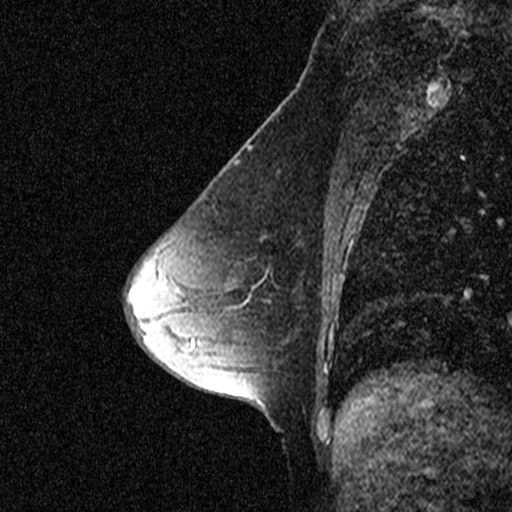
Breast MRI (dynamic contrast-enhanced), one sagittal slice; dynamic contrast-enhanced study with each time point stored as its own series, time point 2 of 3 at this slice position (early post-contrast, ordered by acquisition time); 1.5 T; TE 4.5 ms, TR 11 ms; 2.27 mm slice thickness; 512 × 512 image matrix, field of view 200 × 200 mm. Female patient, age 53 years. Case-level facts recorded for this patient, not image findings: setting: breast cancer imaged before/during neoadjuvant chemotherapy; receptor status: HR-positive, HER2-negative.
Annotated regions visible in this slice (semi-automatic segmentation, software-assisted and operator-edited):
- analysis volume of interest (the breast-tissue region the enhancement analysis was run in; not a lesion): bounding box <200,178,317,309> (left, top, right, bottom; pixels)
- tumour enhancement mask (voxels above the 90 % enhancement threshold inside the analysis volume of interest): <228,288,253,309>